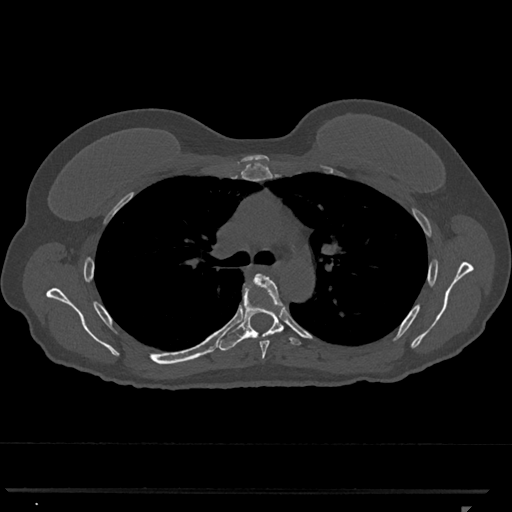
CT including the spine, one axial slice. Slice 782 of 793 in the series (ordered by position). Reconstruction kernel Br40s/3. 120 kVp. Bone window (W 1800 / L 400 HU). 512 × 512 image matrix. Patient: female, 62 years. Case-level facts recorded for this patient, not image findings: primary cancer: renal.
Annotated regions visible in this slice (semi-automatic segmentation, software-assisted and operator-edited):
- T5 vertebra: bounding box <254,274,283,359> (left, top, right, bottom; pixels)
- T6 vertebra: <219,281,301,351>